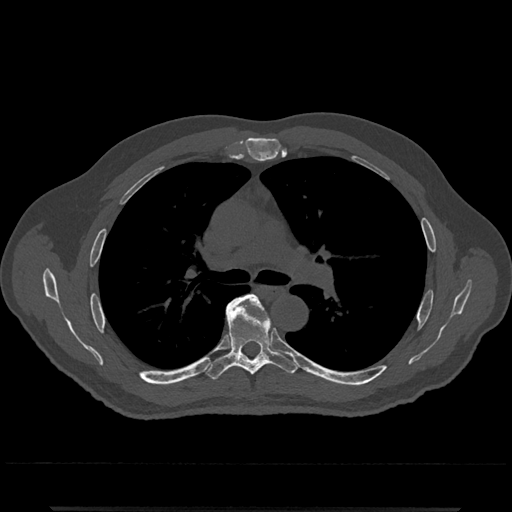
CT including the spine, one axial slice. Reconstruction kernel Br40s/3. Bone window (W 1800 / L 400 HU). 0.5 mm slice thickness. 512 × 512 image matrix. Male patient, age 67 years. From the clinical record (not read from this slice): primary cancer: prostate.
Structures marked on this image (semi-automatic segmentation, software-assisted and operator-edited):
- T5 vertebra: box from (x=237, y=295) to (x=267, y=314) px
- T6 vertebra: (x=206, y=298)–(x=298, y=379)